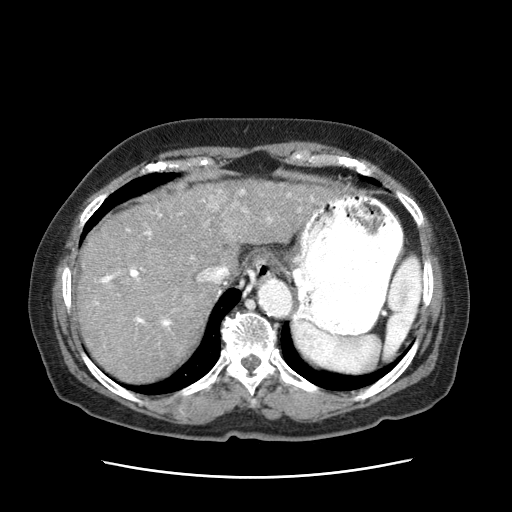
Contrast-enhanced abdominal CT (liver protocol), one axial slice; position 54 of 63 along the scan axis; reconstruction kernel STANDARD; intravenous contrast given; soft-tissue window (W 400 / L 40 HU); 512 × 512 image matrix, field of view 360 × 360 mm. Patient: female, 79 years. From the clinical record (not read from this slice): diagnosis: hepatocellular carcinoma (patient treated with transarterial chemoembolisation; whether this scan precedes or follows treatment is not stated here); TNM stage (as recorded): Stage-II; Child-Pugh class: B; tumour size: 5 cm.
Outlined on this slice (semi-automatically segmented with operator editing):
- abdominal aorta: box from (x=258, y=280) to (x=294, y=318) px
- liver parenchyma outside the tumour (the mass and vessels are separate outlines, so this box may not span the whole liver): (x=76, y=179)–(x=241, y=387)
- mass: (x=206, y=179)–(x=333, y=244)
- liver vessels: (x=94, y=204)–(x=248, y=327)